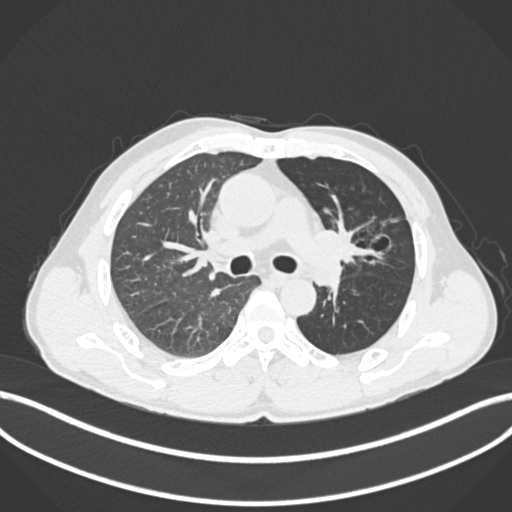
Chest CT, one axial slice; slice 118 of 255 in the series (ordered by position); 120 kVp; lung window (W 1500 / L -600 HU); 1 mm slice thickness; 512 × 512 image matrix, field of view 400 × 400 mm. Male patient, age 57 years. From the clinical record (not read from this slice): clinical TNM (as recorded): T2b N0 M0.
Outlined on this slice (rectangle marked by the reading radiologist):
- lung tumour (recorded histology: squamous cell carcinoma): bounding box <315,222,371,268> (left, top, right, bottom; pixels)